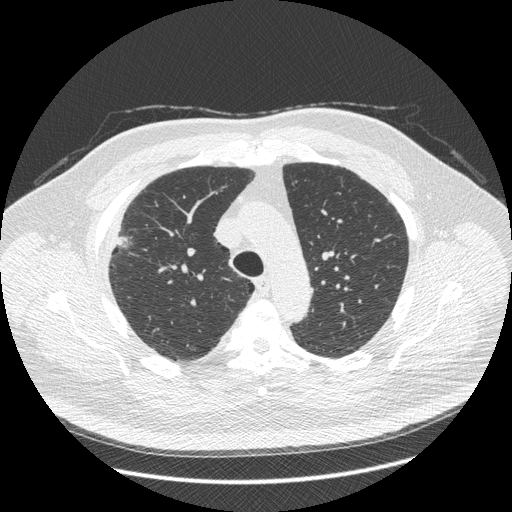
Chest CT (low-dose screening protocol), one axial image; third annual screen; lung window (W 1500 / L -600 HU); 1.25 mm slice thickness; 120 kVp; slice 111 of 426 in the series. Male, age 66 years at enrolment. Current smoker at enrolment.
Expert-annotated lung lesion, box from (x=88, y=212) to (x=148, y=271) px. The exam's reader record, not a measurement of the box and not confirmed to be the same lesion: non-calcified nodule or mass ≥4 mm, right upper lobe, 48 × 25 mm, spiculated (stellate) margins, soft tissue attenuation, pre-existing on the prior screen: no. Official screen result: positive, other. Lung cancer was diagnosed 35 days after this screen: non-small cell carcinoma, right upper lobe, stage IV (AJCC 6th edition), 50 mm at pathology.